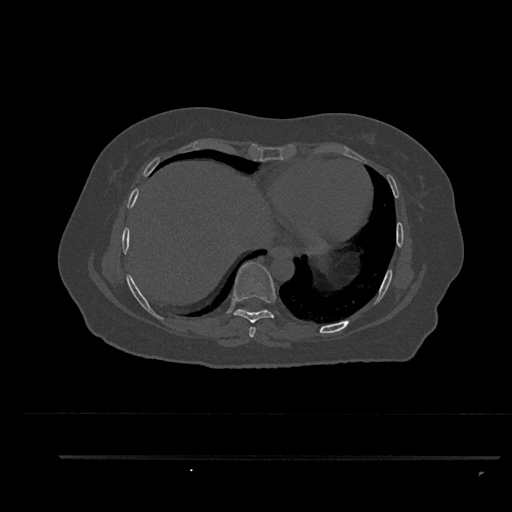
CT including the spine, one axial slice. Slice 455 of 797 in the series (ordered by position). 120 kVp. Bone window (W 1800 / L 400 HU). 512 × 512 image matrix, field of view 408 × 408 mm. Patient: female, 44 years. Case-level facts recorded for this patient, not image findings: primary cancer: renal; vertebrae with lytic lesions (as recorded): L1.
Annotated regions visible in this slice (semi-automatic segmentation, software-assisted and operator-edited):
- T7 vertebra: box from (x=249, y=327) to (x=256, y=338) px
- T8 vertebra: (x=233, y=262)–(x=276, y=323)
- T9 vertebra: (x=237, y=309)–(x=263, y=311)